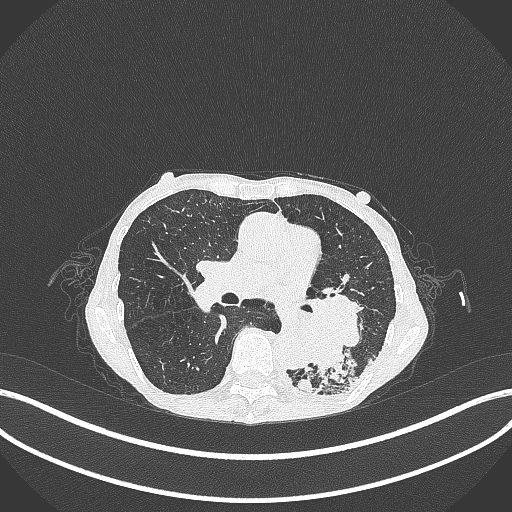
Chest CT, one axial slice; position 144 of 347 along the scan axis; 120 kVp; lung window (W 1500 / L -600 HU); 1 mm slice thickness; 512 × 512 image matrix, field of view 400 × 400 mm. Patient: female, 70 years. Case-level facts recorded for this patient, not image findings: clinical TNM (as recorded): T3 N0 M0.
Outlined on this slice (bounding box drawn by a radiologist):
- lung tumour (recorded histology: small cell carcinoma): bounding box <294,286,357,377> (left, top, right, bottom; pixels)